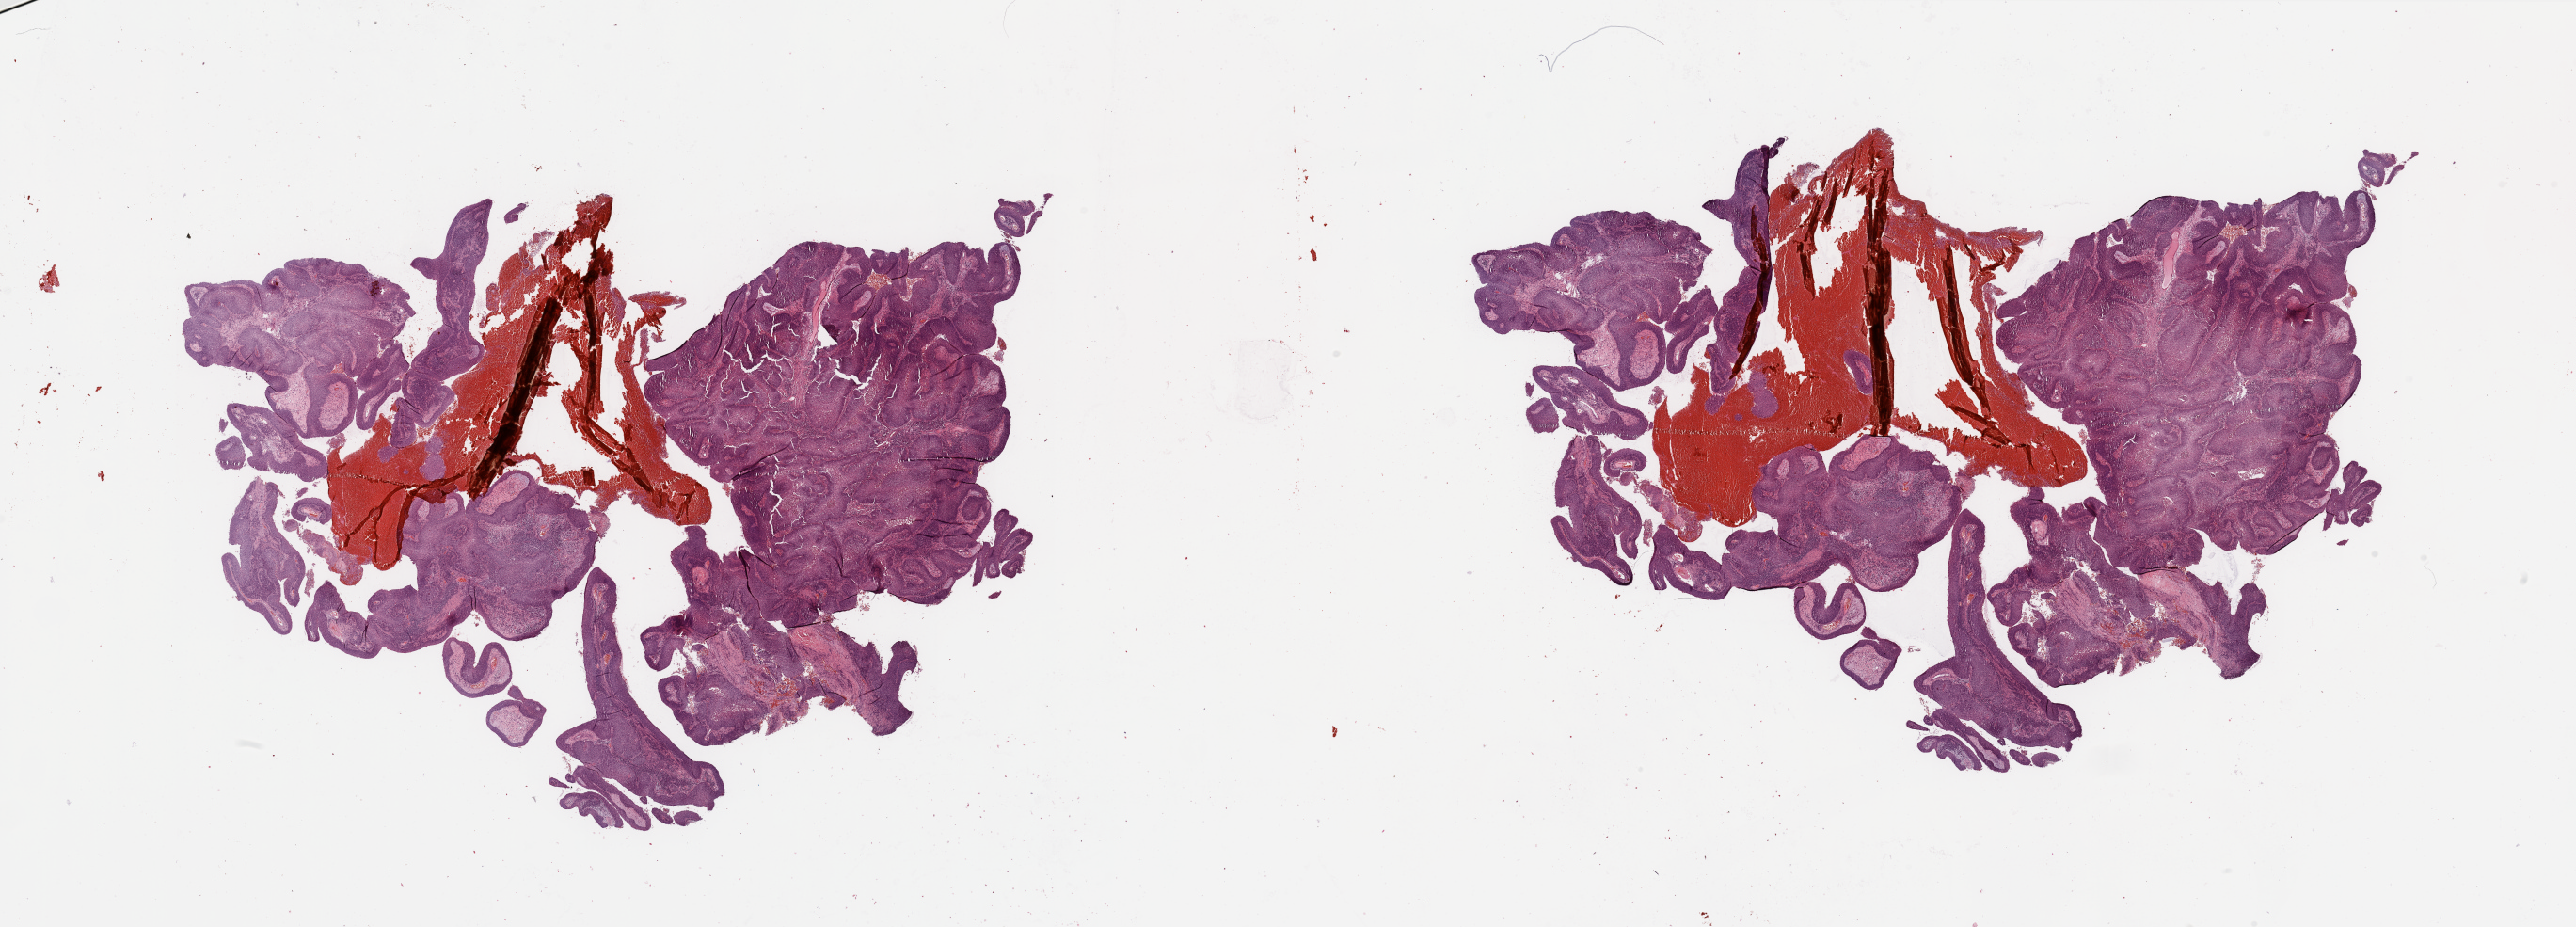
Digitized H&E-stained tissue section (whole slide) — low-resolution overview of the scanned area, about 43.3 x 15.6 mm (slide scanned at 20x). Lung, tumour tissue. 68-year-old male patient.
Patient diagnosis (cohort enrolment): squamous cell carcinoma (lung).